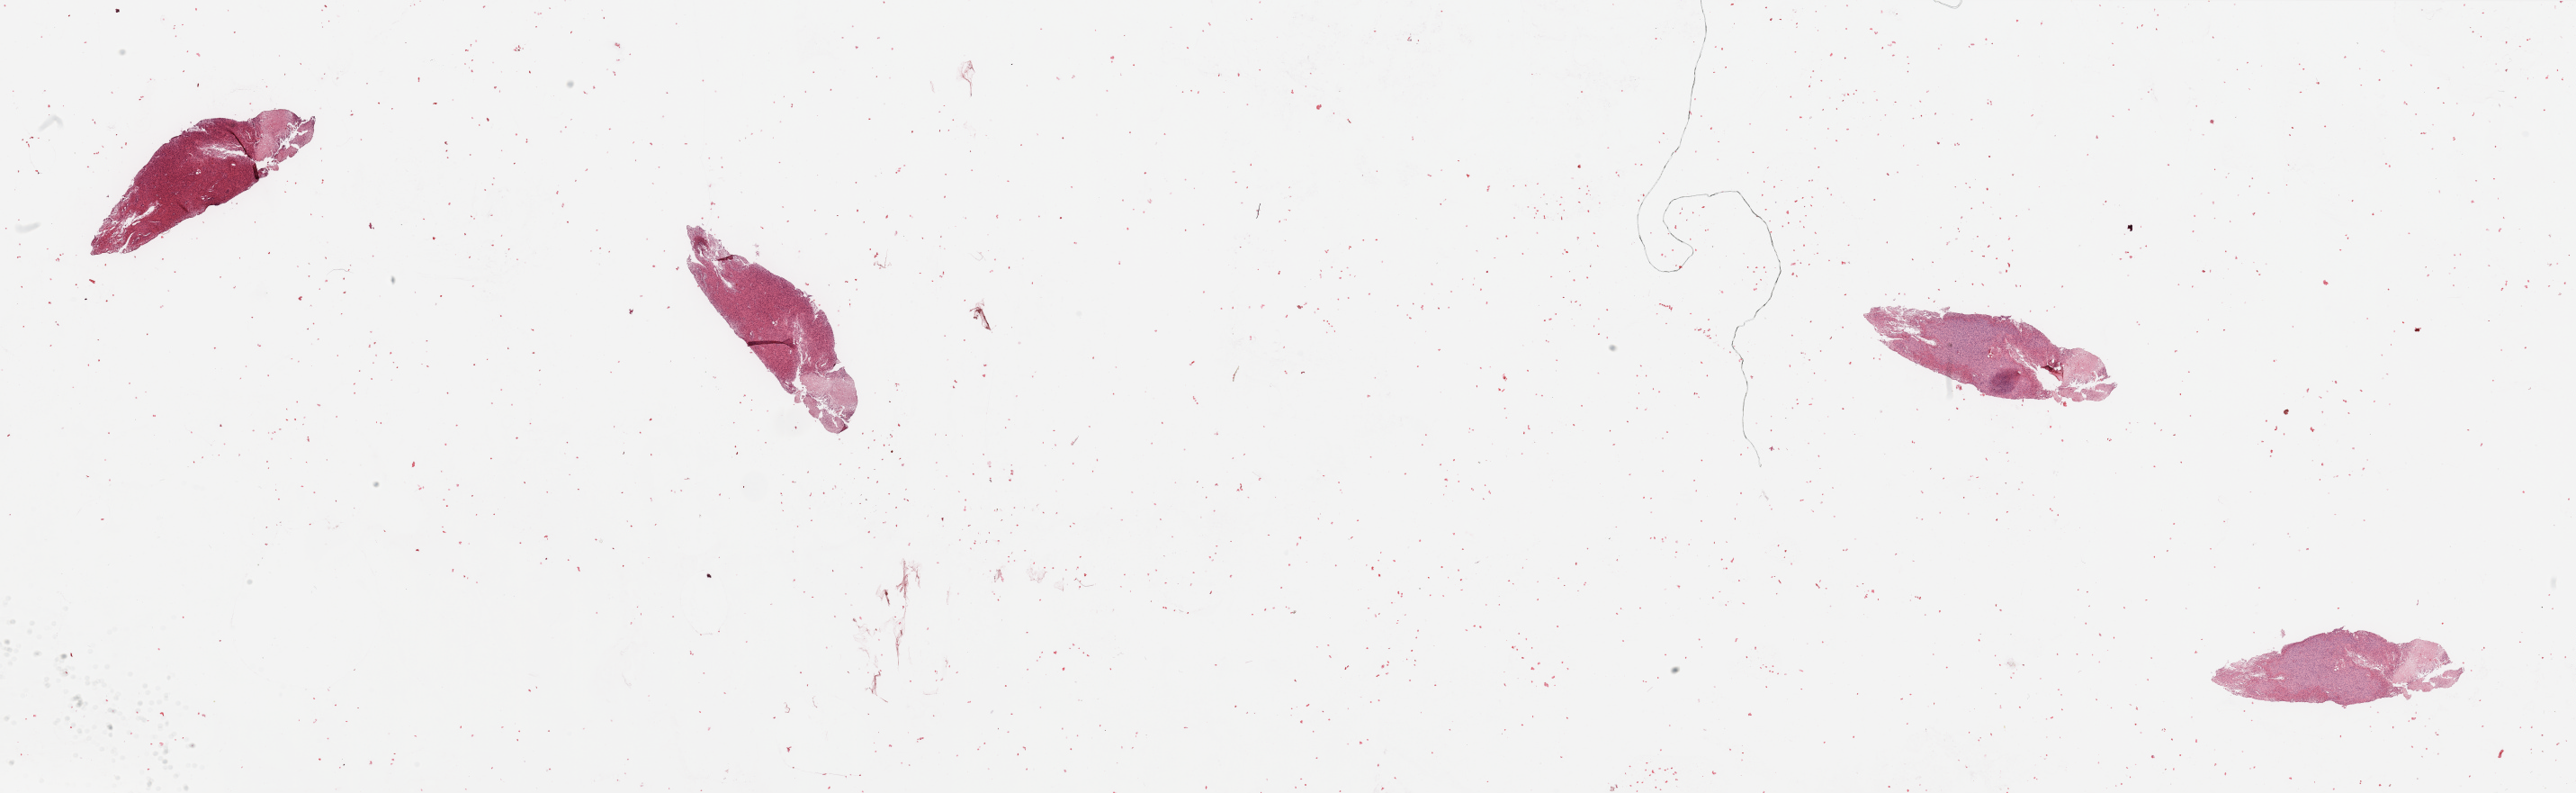
Whole-slide histology image, H&E-stained, whole scanned area (about 45.3 x 13.9 mm, slide scanned at 20x) shown as a low-resolution overview; brain, tumour tissue. Female, 64 y/o.
* histologic diagnosis: Glioblastoma
* primary tumour site (as recorded): occipital lobe